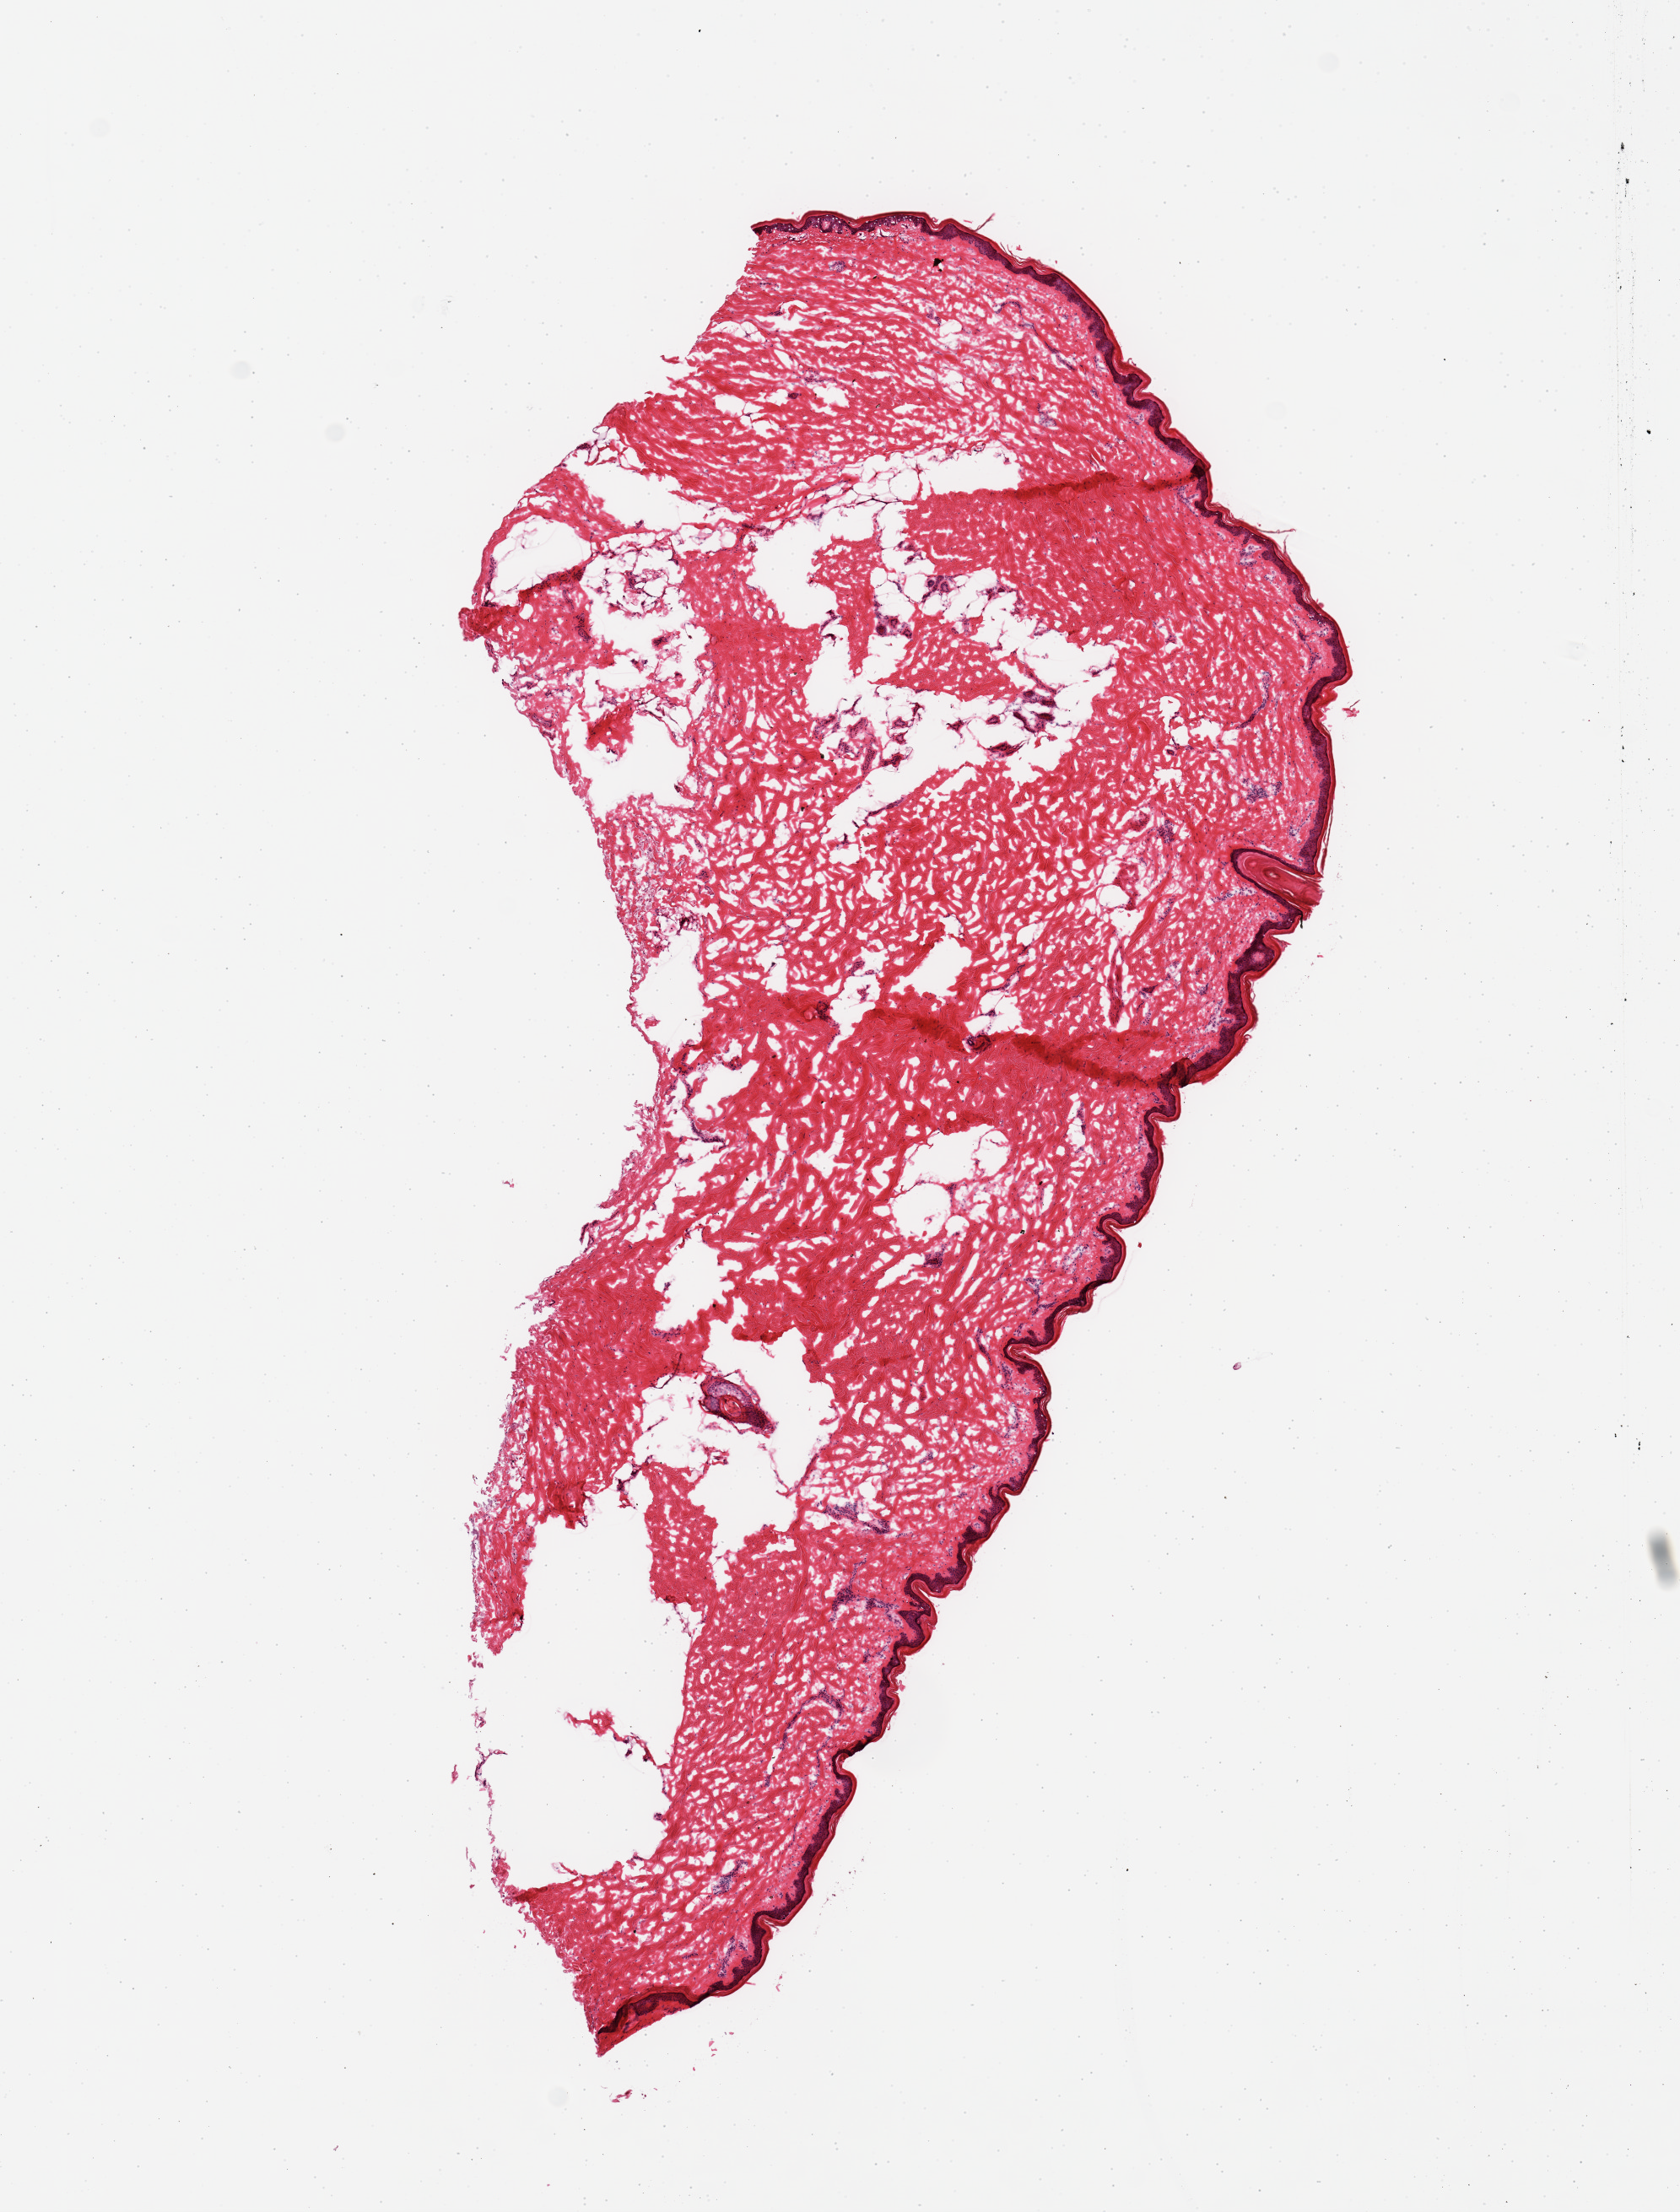
Hematoxylin and eosin (H&E) whole-slide image, brightfield, whole scanned area (about 7.9 x 10.4 mm) shown as a low-resolution overview. Frozen section (dry ice). Section of skin of lower leg (target tissue). Donor tissue sample. Donor sex: female.
Reviewer comment on this tissue sample: 1 piece.